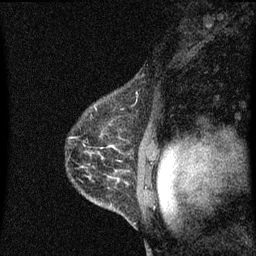
Breast MRI (dynamic contrast-enhanced), one sagittal slice; position 48 of 60 along the scan axis; dynamic contrast-enhanced series, image 2 of 3 at this slice position (ordered by acquisition); 1.5 T; TE 4.2 ms, TR 8.4 ms; 2 mm slice thickness; 256 × 256 image matrix, field of view 200 × 200 mm. Female patient, age 41 years.
Structures marked on this image (semi-automatic segmentation, software-assisted and operator-edited):
- analysis volume of interest (the breast-tissue region the enhancement analysis was run in; not a lesion): box from (x=121, y=74) to (x=145, y=99) px
- tumour enhancement mask (voxels above the 70 % enhancement threshold inside the analysis volume of interest): (x=137, y=92)–(x=139, y=99)